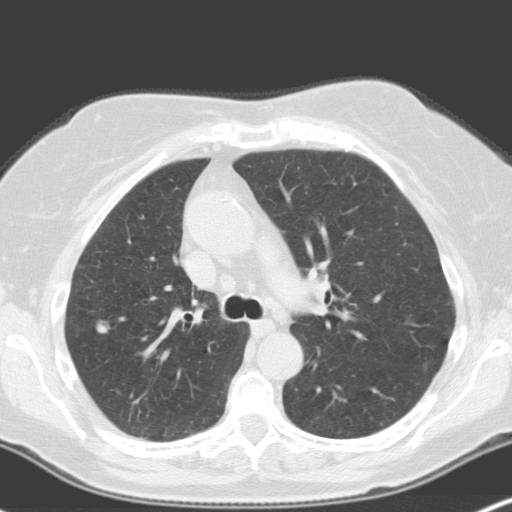
Low-dose screening chest CT, one axial slice; slice 115 of 160 in the series (ordered by position); lung window (W 1500 / L -600 HU); 512 × 512 image matrix.
Structures marked on this image (expert manual segmentation):
- lesion 3 (nodule): box from (x=96, y=321) to (x=109, y=333) px